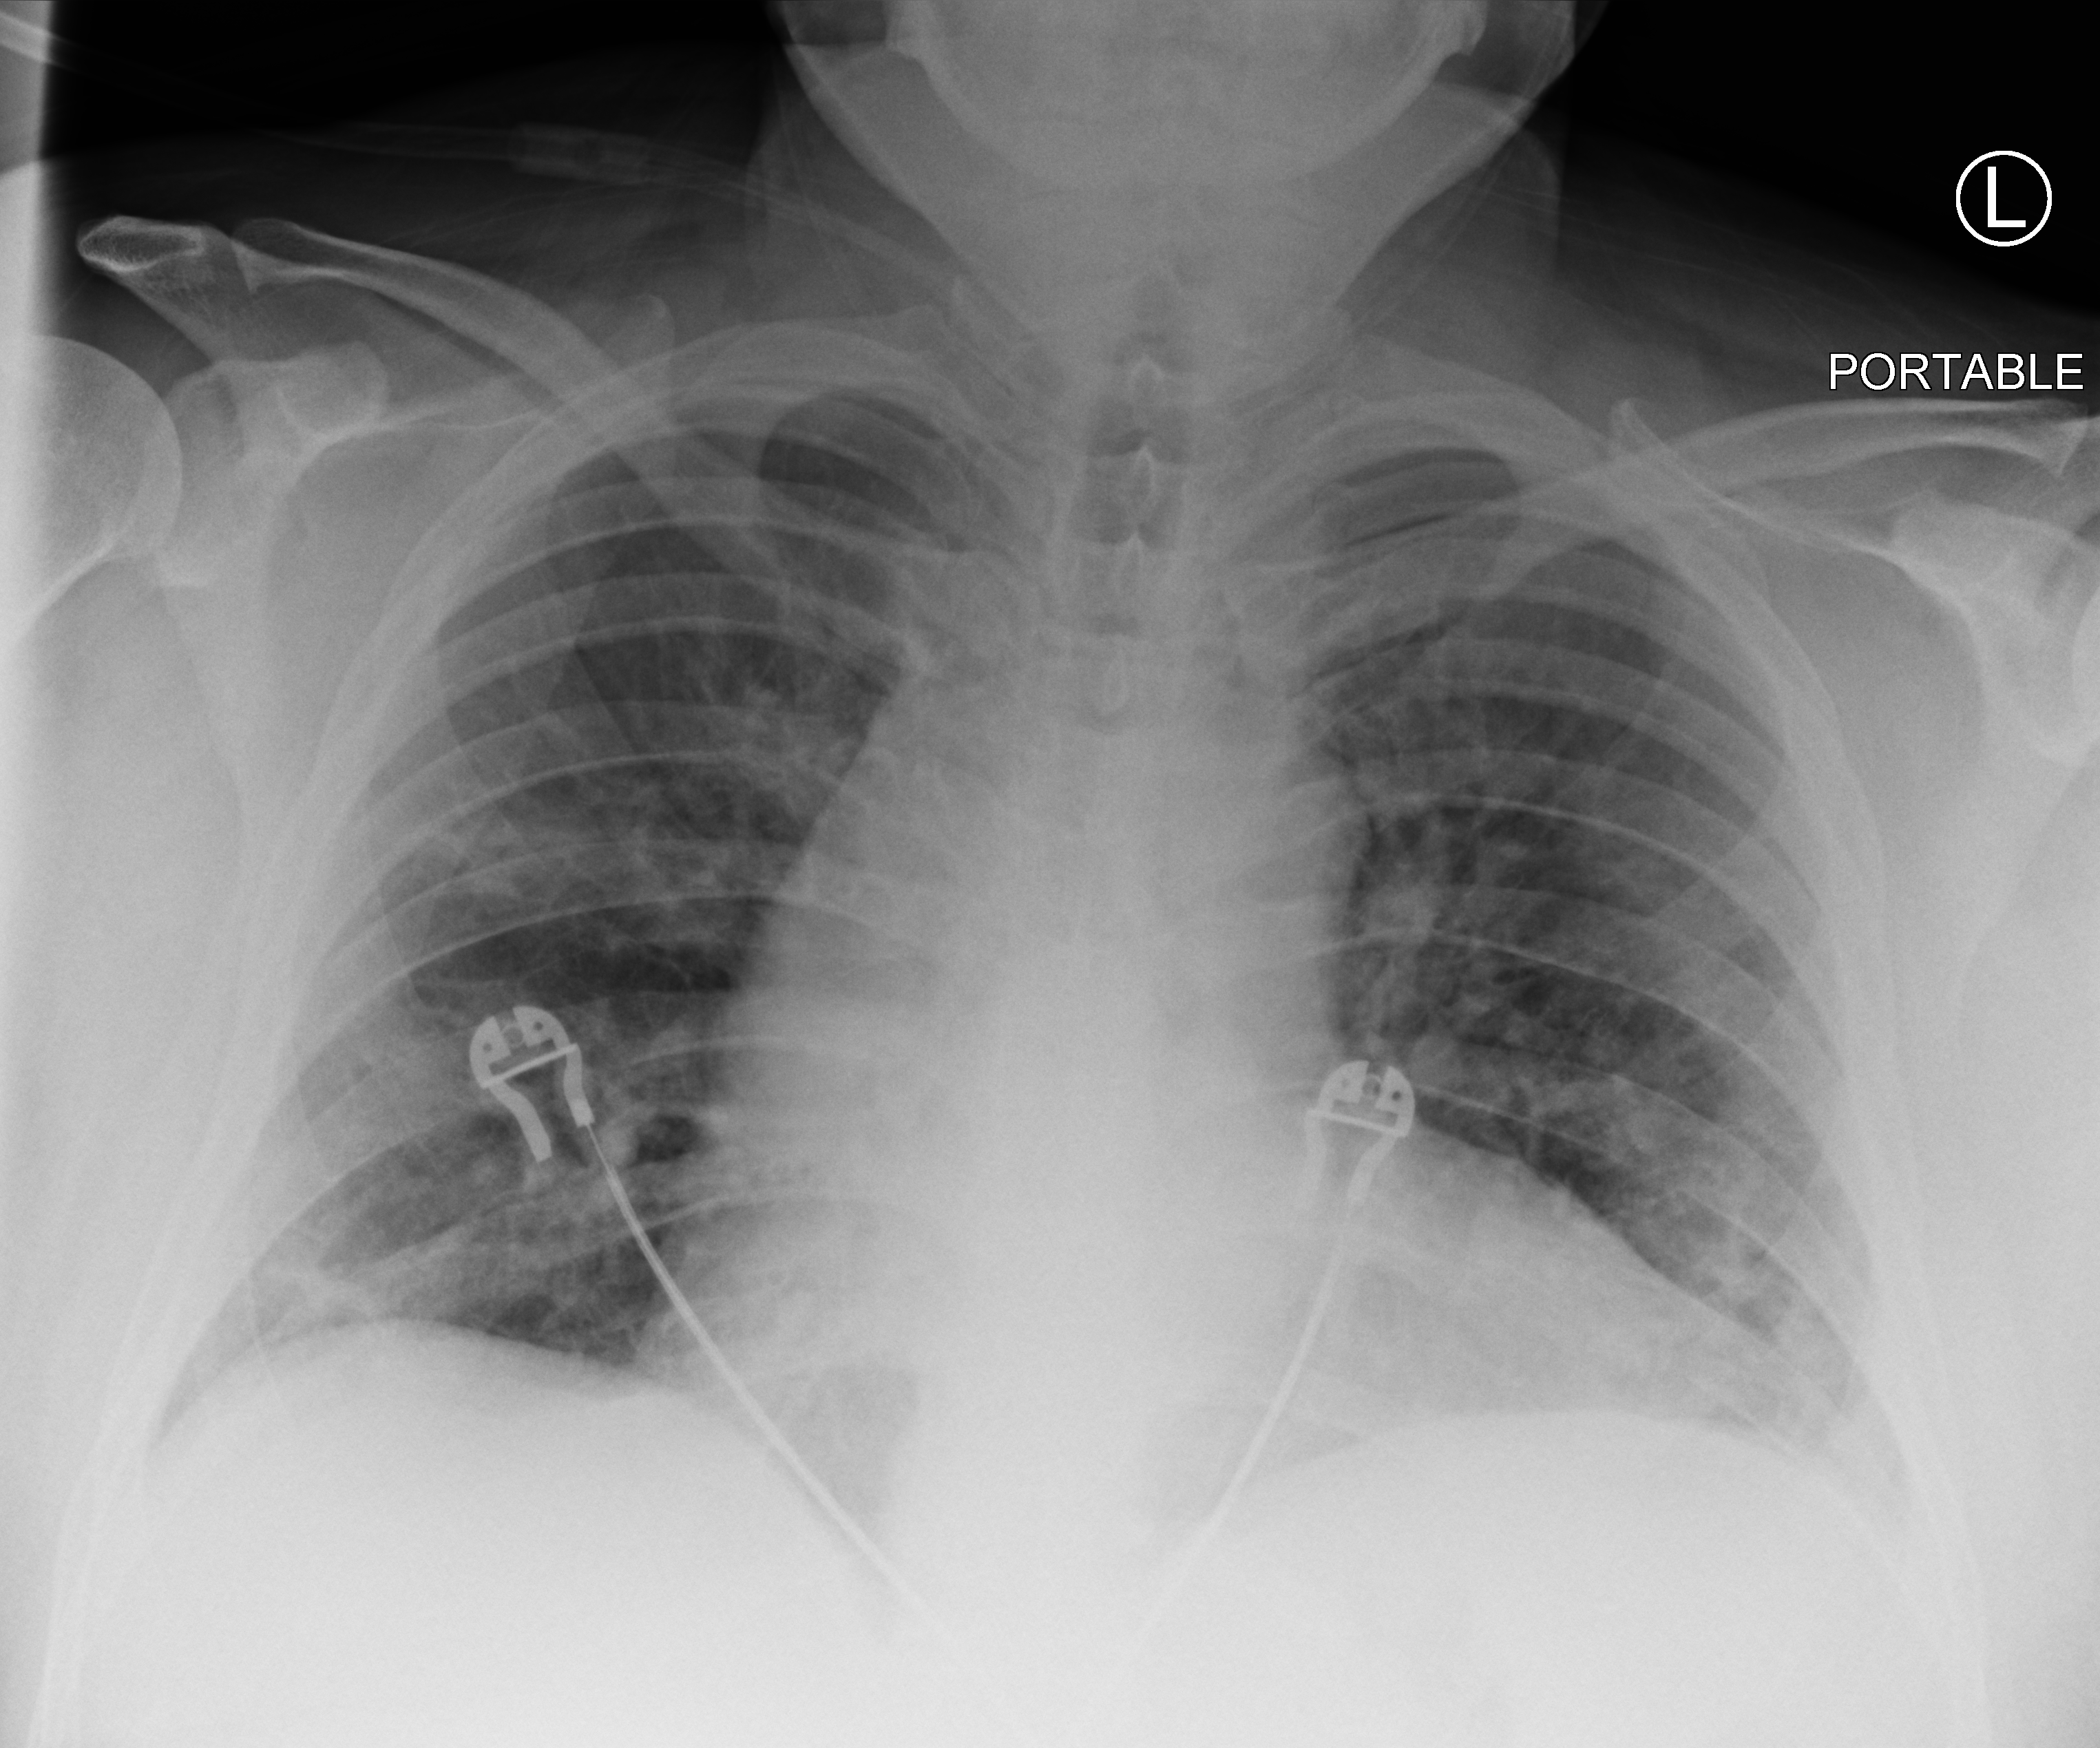
Portable chest radiograph. Patient hospitalised with COVID-19; male, aged 18–59 years.
From the hospital-stay record, not from the radiograph (when in the stay this image was taken is not recorded):
- smoking status (admission record): current
- mechanically ventilated during this hospital stay: no
- admitted to intensive care during this hospital stay: no